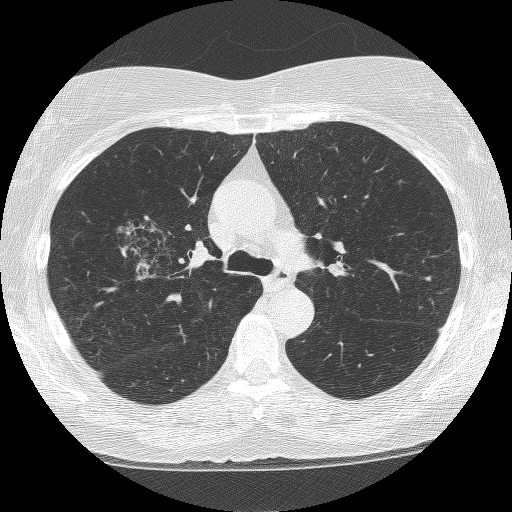
Low-dose screening chest CT, axial slice. Second annual screen. Lung window (W 1500 / L -600 HU). Lung (sharp) reconstruction kernel (BONE). 512 × 512 image matrix. Female, age 64 years at enrolment.
Lesion marked by an expert reader, bounding box [x1, y1, x2, y2] px = [114, 204, 209, 293]. The screening reader recorded 4 non-calcified nodules or masses ≥4 mm on this exam (right upper lobe, right upper lobe, right upper lobe, left upper lobe); which of them this box marks is not recorded. Later outcome: lung cancer diagnosed 381 days after this screen — adenocarcinoma, NOS, right upper lobe, right middle lobe, right hilum, stage IV (AJCC 6th edition), 85 mm at pathology.